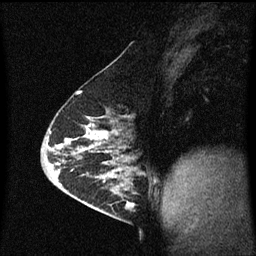
Breast MRI (dynamic contrast-enhanced), one sagittal slice. Position 32 of 60 along the scan axis. Dynamic contrast-enhanced series, image 2 of 3 at this slice position (ordered by acquisition). 1.5 T. TE 4.2 ms, TR 8.4 ms. 2 mm slice thickness. 256 × 256 image matrix, field of view 200 × 200 mm. Female patient, age 63 years.
Annotated regions visible in this slice (semi-automatically segmented with operator editing):
- analysis volume of interest (the breast-tissue region the enhancement analysis was run in; not a lesion): bounding box [x1, y1, x2, y2] px = [98, 168, 145, 217]
- tumour enhancement mask (voxels above the 70 % enhancement threshold inside the analysis volume of interest): [102, 168, 141, 209]